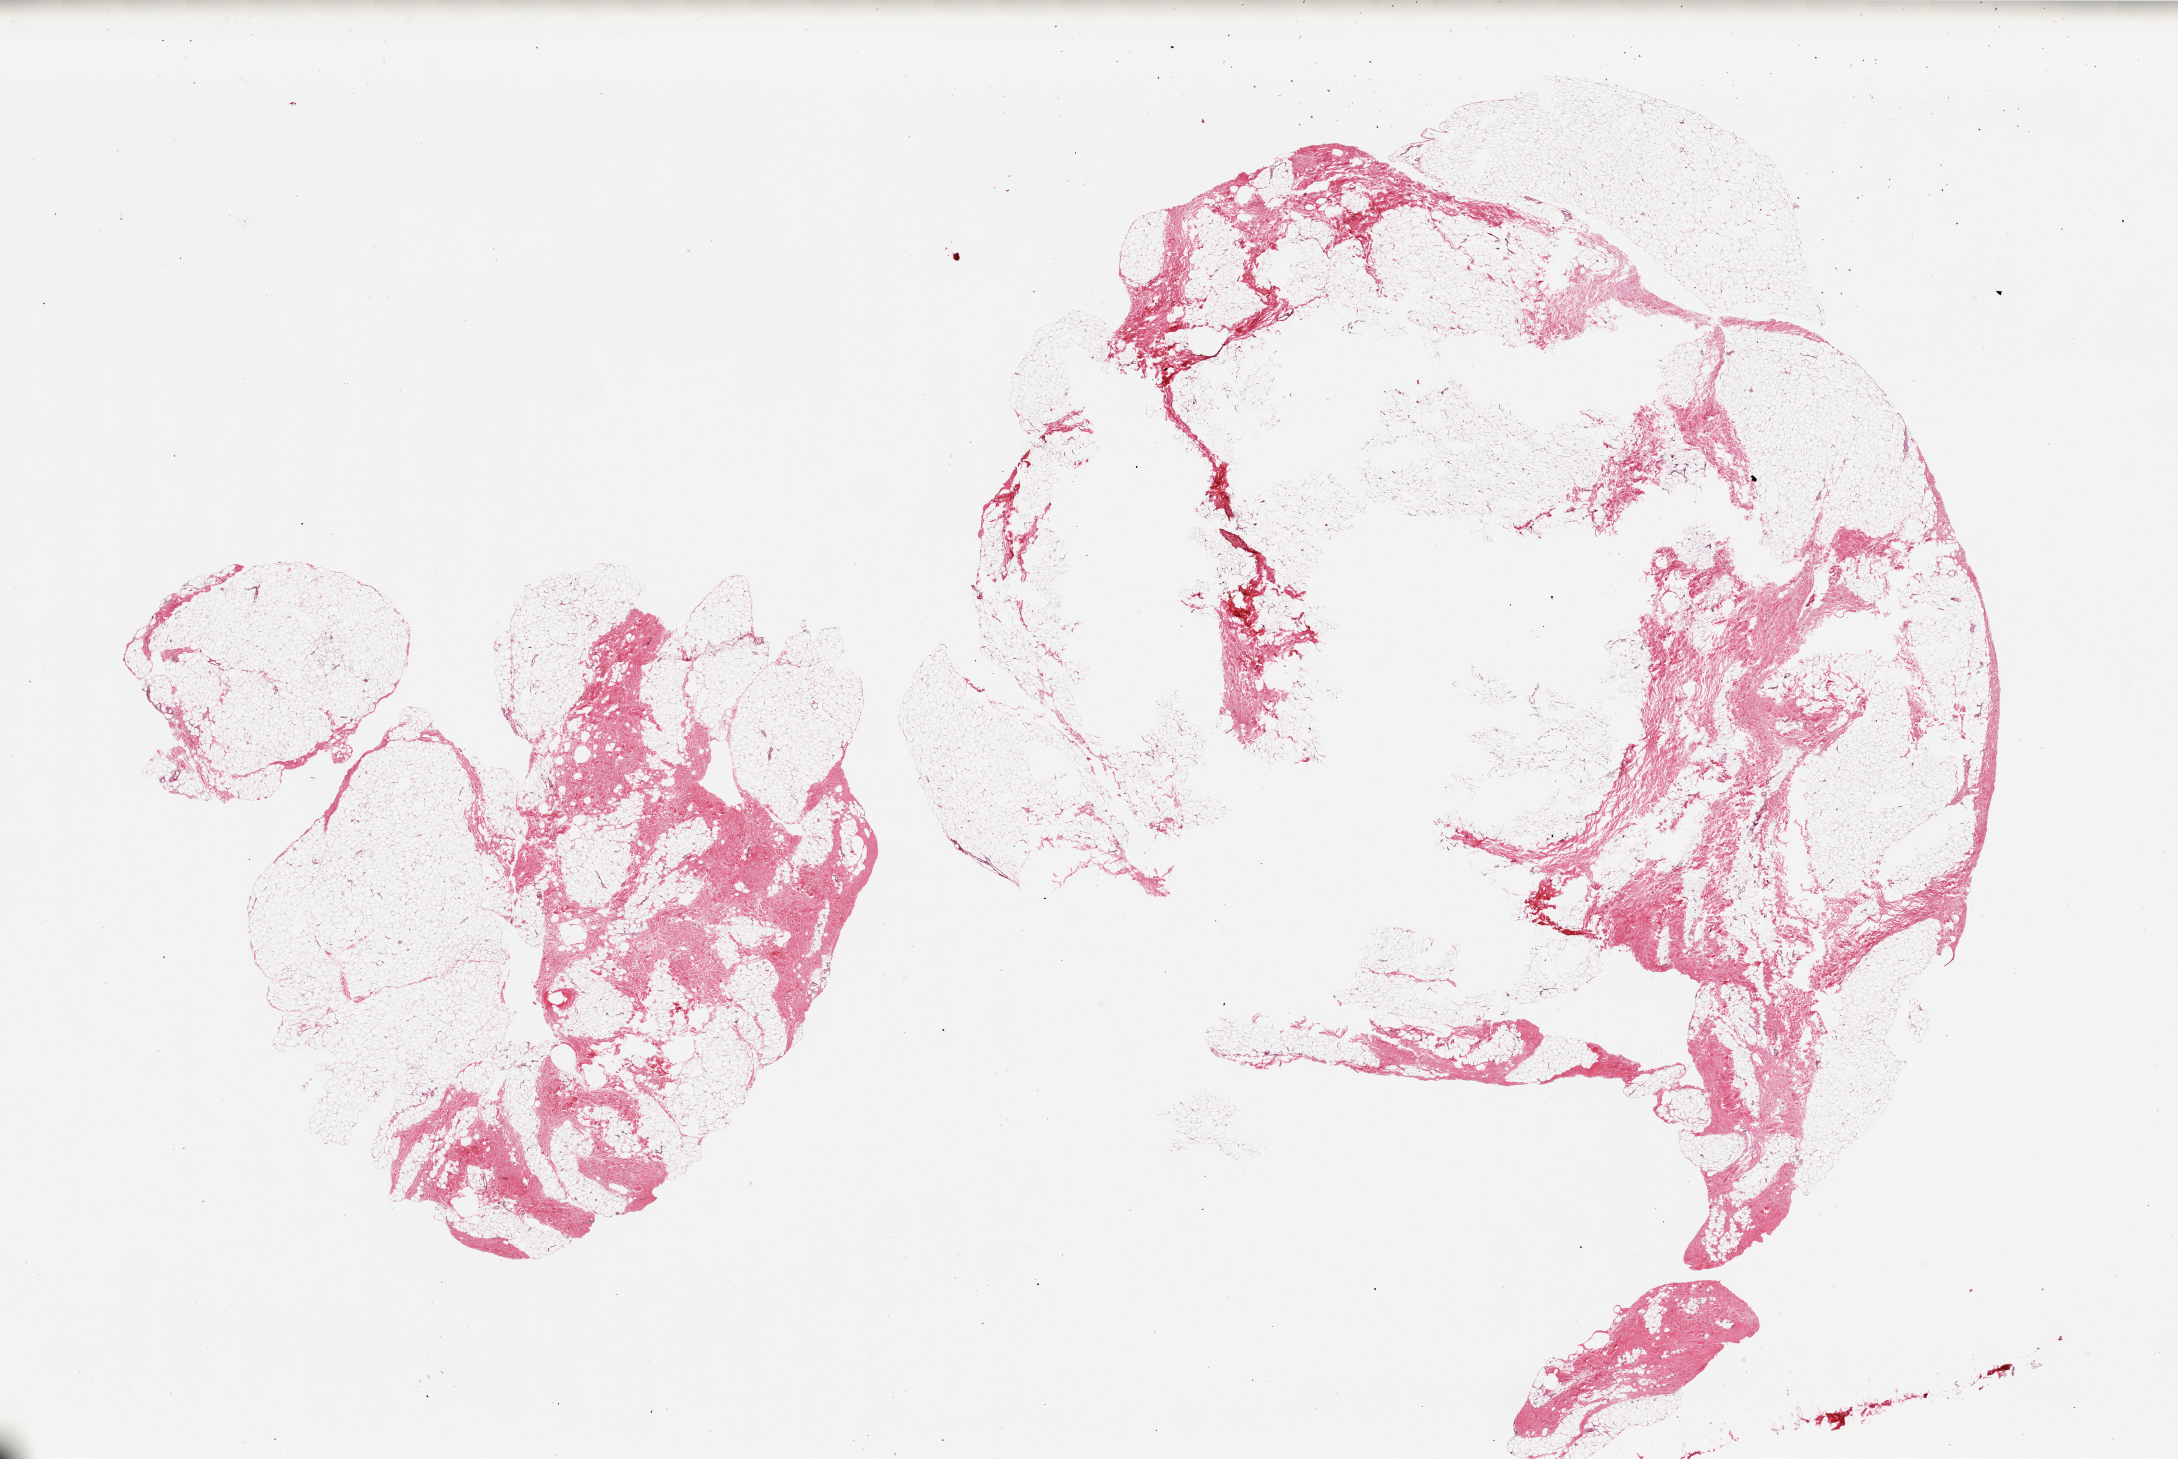
Hematoxylin and eosin (H&E) whole-slide image, brightfield, whole scanned area (about 34.5 x 23.1 mm) shown as a low-resolution overview. PAXgene-fixed, paraffin-embedded tissue. Sampled site (target tissue): breast. Tissue donor sample. Donor: male.
Reviewer comment on this tissue sample: 2 pieces. Overly large pieces of fibroadipose tissue with central defects (holes).